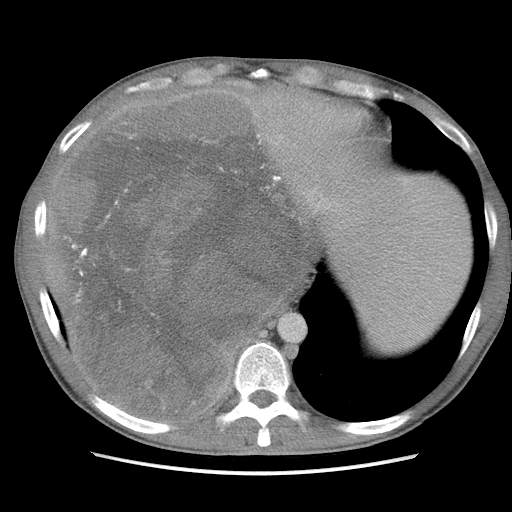
Contrast-enhanced abdominal CT, one axial slice. Slice 88 of 115 in the series (ordered by position). Soft-tissue window (W 400 / L 40 HU). 512 × 512 image matrix, field of view 360 × 360 mm. Male patient. From the clinical record (not read from this slice): diagnosis: adrenocortical carcinoma; tumour side: right adrenal; Ki-67 index: 13 %; stage (as recorded): 3.
Outlined on this slice (semi-automatic segmentation, software-assisted and operator-edited):
- mass: box from (x=59, y=95) to (x=297, y=420) px